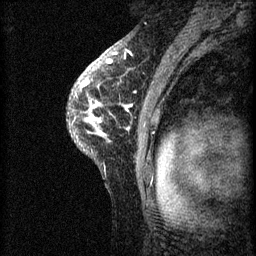
Breast MRI (dynamic contrast-enhanced), one sagittal slice; position 47 of 60 along the scan axis; 3 images stored at this slice position (order not interpretable as contrast timing); 1.5 T; TE 4.2 ms, TR 8.2 ms; 2 mm slice thickness; 256 × 256 image matrix, field of view 180 × 180 mm. Female patient, age 41 years.
Outlined on this slice (semi-automatically segmented with operator editing):
- analysis volume of interest (the breast-tissue region the enhancement analysis was run in; not a lesion): bounding box [x1, y1, x2, y2] px = [67, 62, 160, 175]
- tumour enhancement mask (voxels above the 70 % enhancement threshold inside the analysis volume of interest): [75, 62, 132, 137]